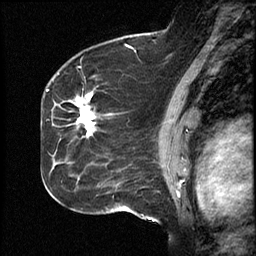
Breast MRI (dynamic contrast-enhanced), one sagittal slice; slice 30 of 46 in the series (ordered by position); dynamic contrast-enhanced study with each time point stored as its own series, time point 2 of 4 at this slice position (early post-contrast, ordered by acquisition time); 1.5 T; TE 4.2 ms, TR 18.3 ms; 3 mm slice thickness; 256 × 256 image matrix, field of view 200 × 200 mm. From the clinical record (not read from this slice): setting: breast cancer imaged before/during neoadjuvant chemotherapy; receptor status: HR-positive, HER2-negative.
Outlined on this slice (semi-automatic segmentation, software-assisted and operator-edited):
- analysis volume of interest (the breast-tissue region the enhancement analysis was run in; not a lesion): bounding box (x1, y1, x2, y2) in pixels: (64, 77, 111, 195)
- tumour enhancement mask (voxels above the 100 % enhancement threshold inside the analysis volume of interest): (77, 96, 95, 135)